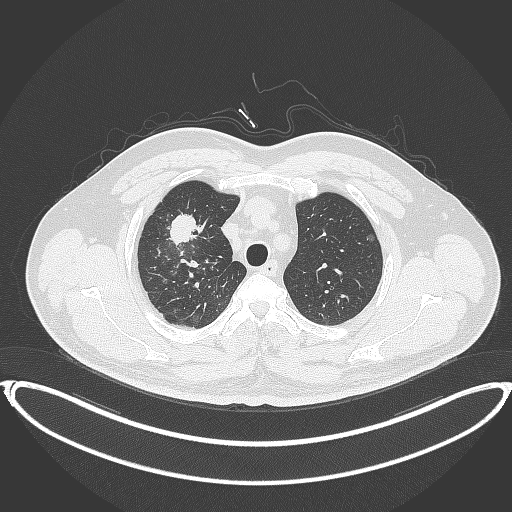
Chest CT, one axial slice; position 311 of 399 along the scan axis; 120 kVp; lung window (W 1500 / L -600 HU); 1 mm slice thickness; 512 × 512 image matrix, field of view 445 × 445 mm. Male patient, age 53 years. From the clinical record (not read from this slice): clinical TNM (as recorded): T2a N0 M0.
Outlined on this slice (bounding box drawn by a radiologist):
- lung tumour (recorded histology: adenocarcinoma): bounding box (x1, y1, x2, y2) in pixels: (166, 208, 206, 246)